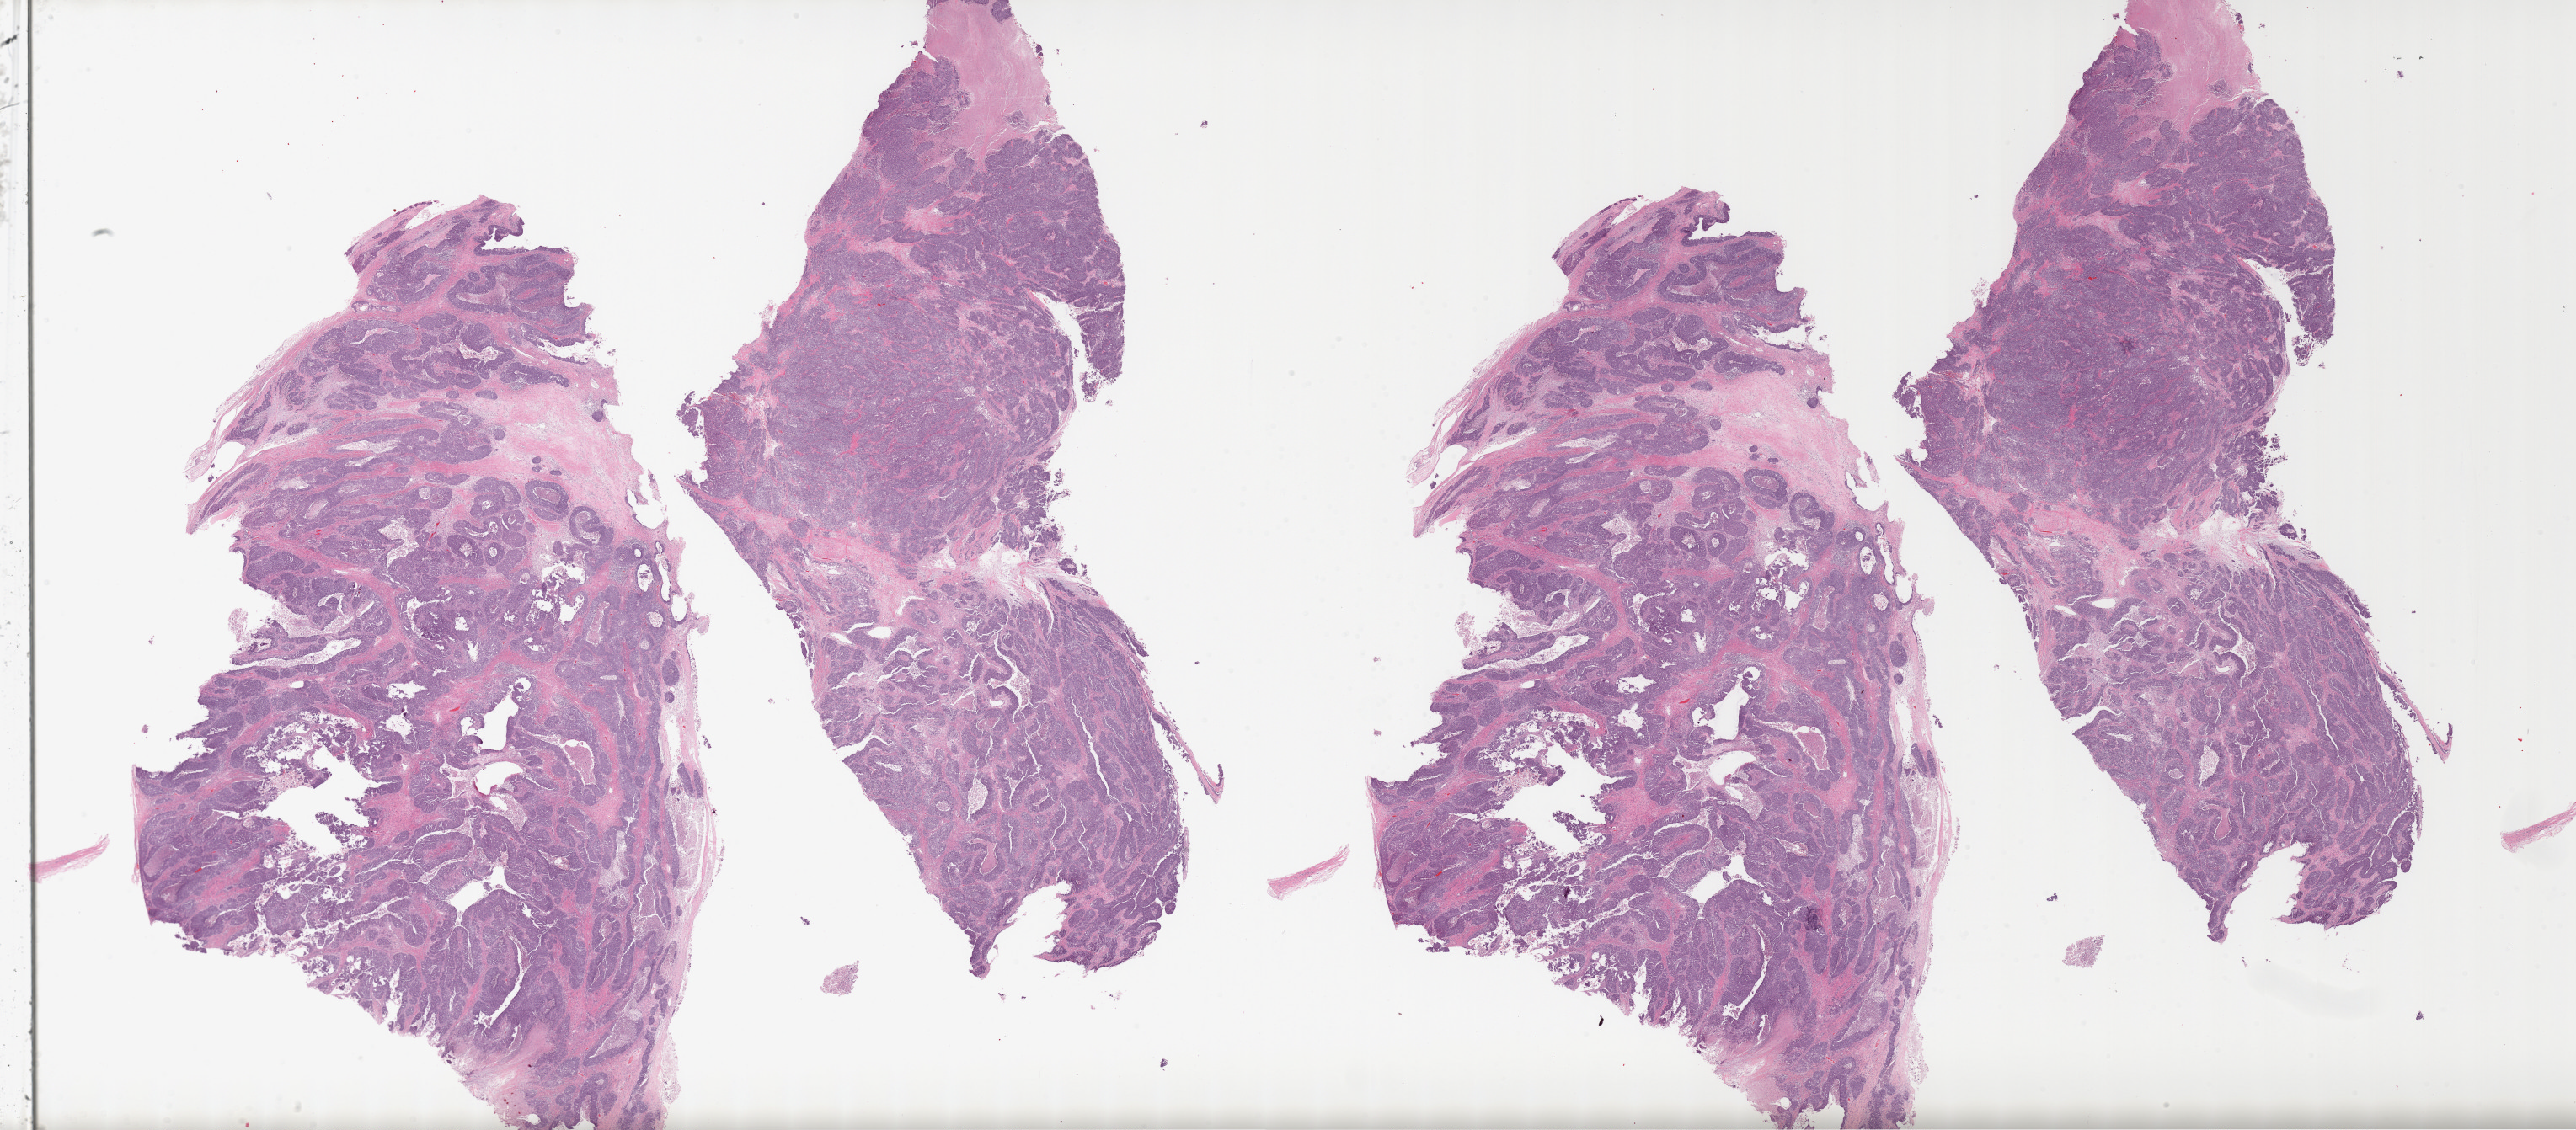
Whole-slide histology image, H&E-stained, shown as a low-resolution overview of the whole scanned area (about 48.7 x 21.4 mm, from a 20x scan). Formalin-fixed paraffin-embedded (FFPE) diagnostic section. Primary tumour sample from the ovary. Patient: female, age at initial diagnosis 67 years. Histologic grade: G3 (poorly differentiated).
• histologic diagnosis: Serous cystadenocarcinoma, NOS
• laterality: bilateral
• FIGO stage: IIIC